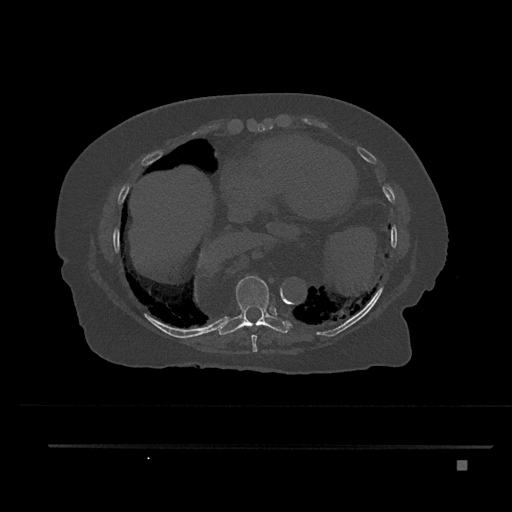
CT including the spine, one axial slice; position 409 of 797 along the scan axis; reconstruction kernel Br40s/3; bone window (W 1800 / L 400 HU); 512 × 512 image matrix, field of view 437 × 437 mm. Patient: female, 76 years. Case-level facts recorded for this patient, not image findings: primary cancer: lung.
Outlined on this slice (semi-automatically segmented with operator editing):
- T8 vertebra: bounding box [x1, y1, x2, y2] px = [251, 335, 257, 352]
- T9 vertebra: [216, 276, 290, 335]